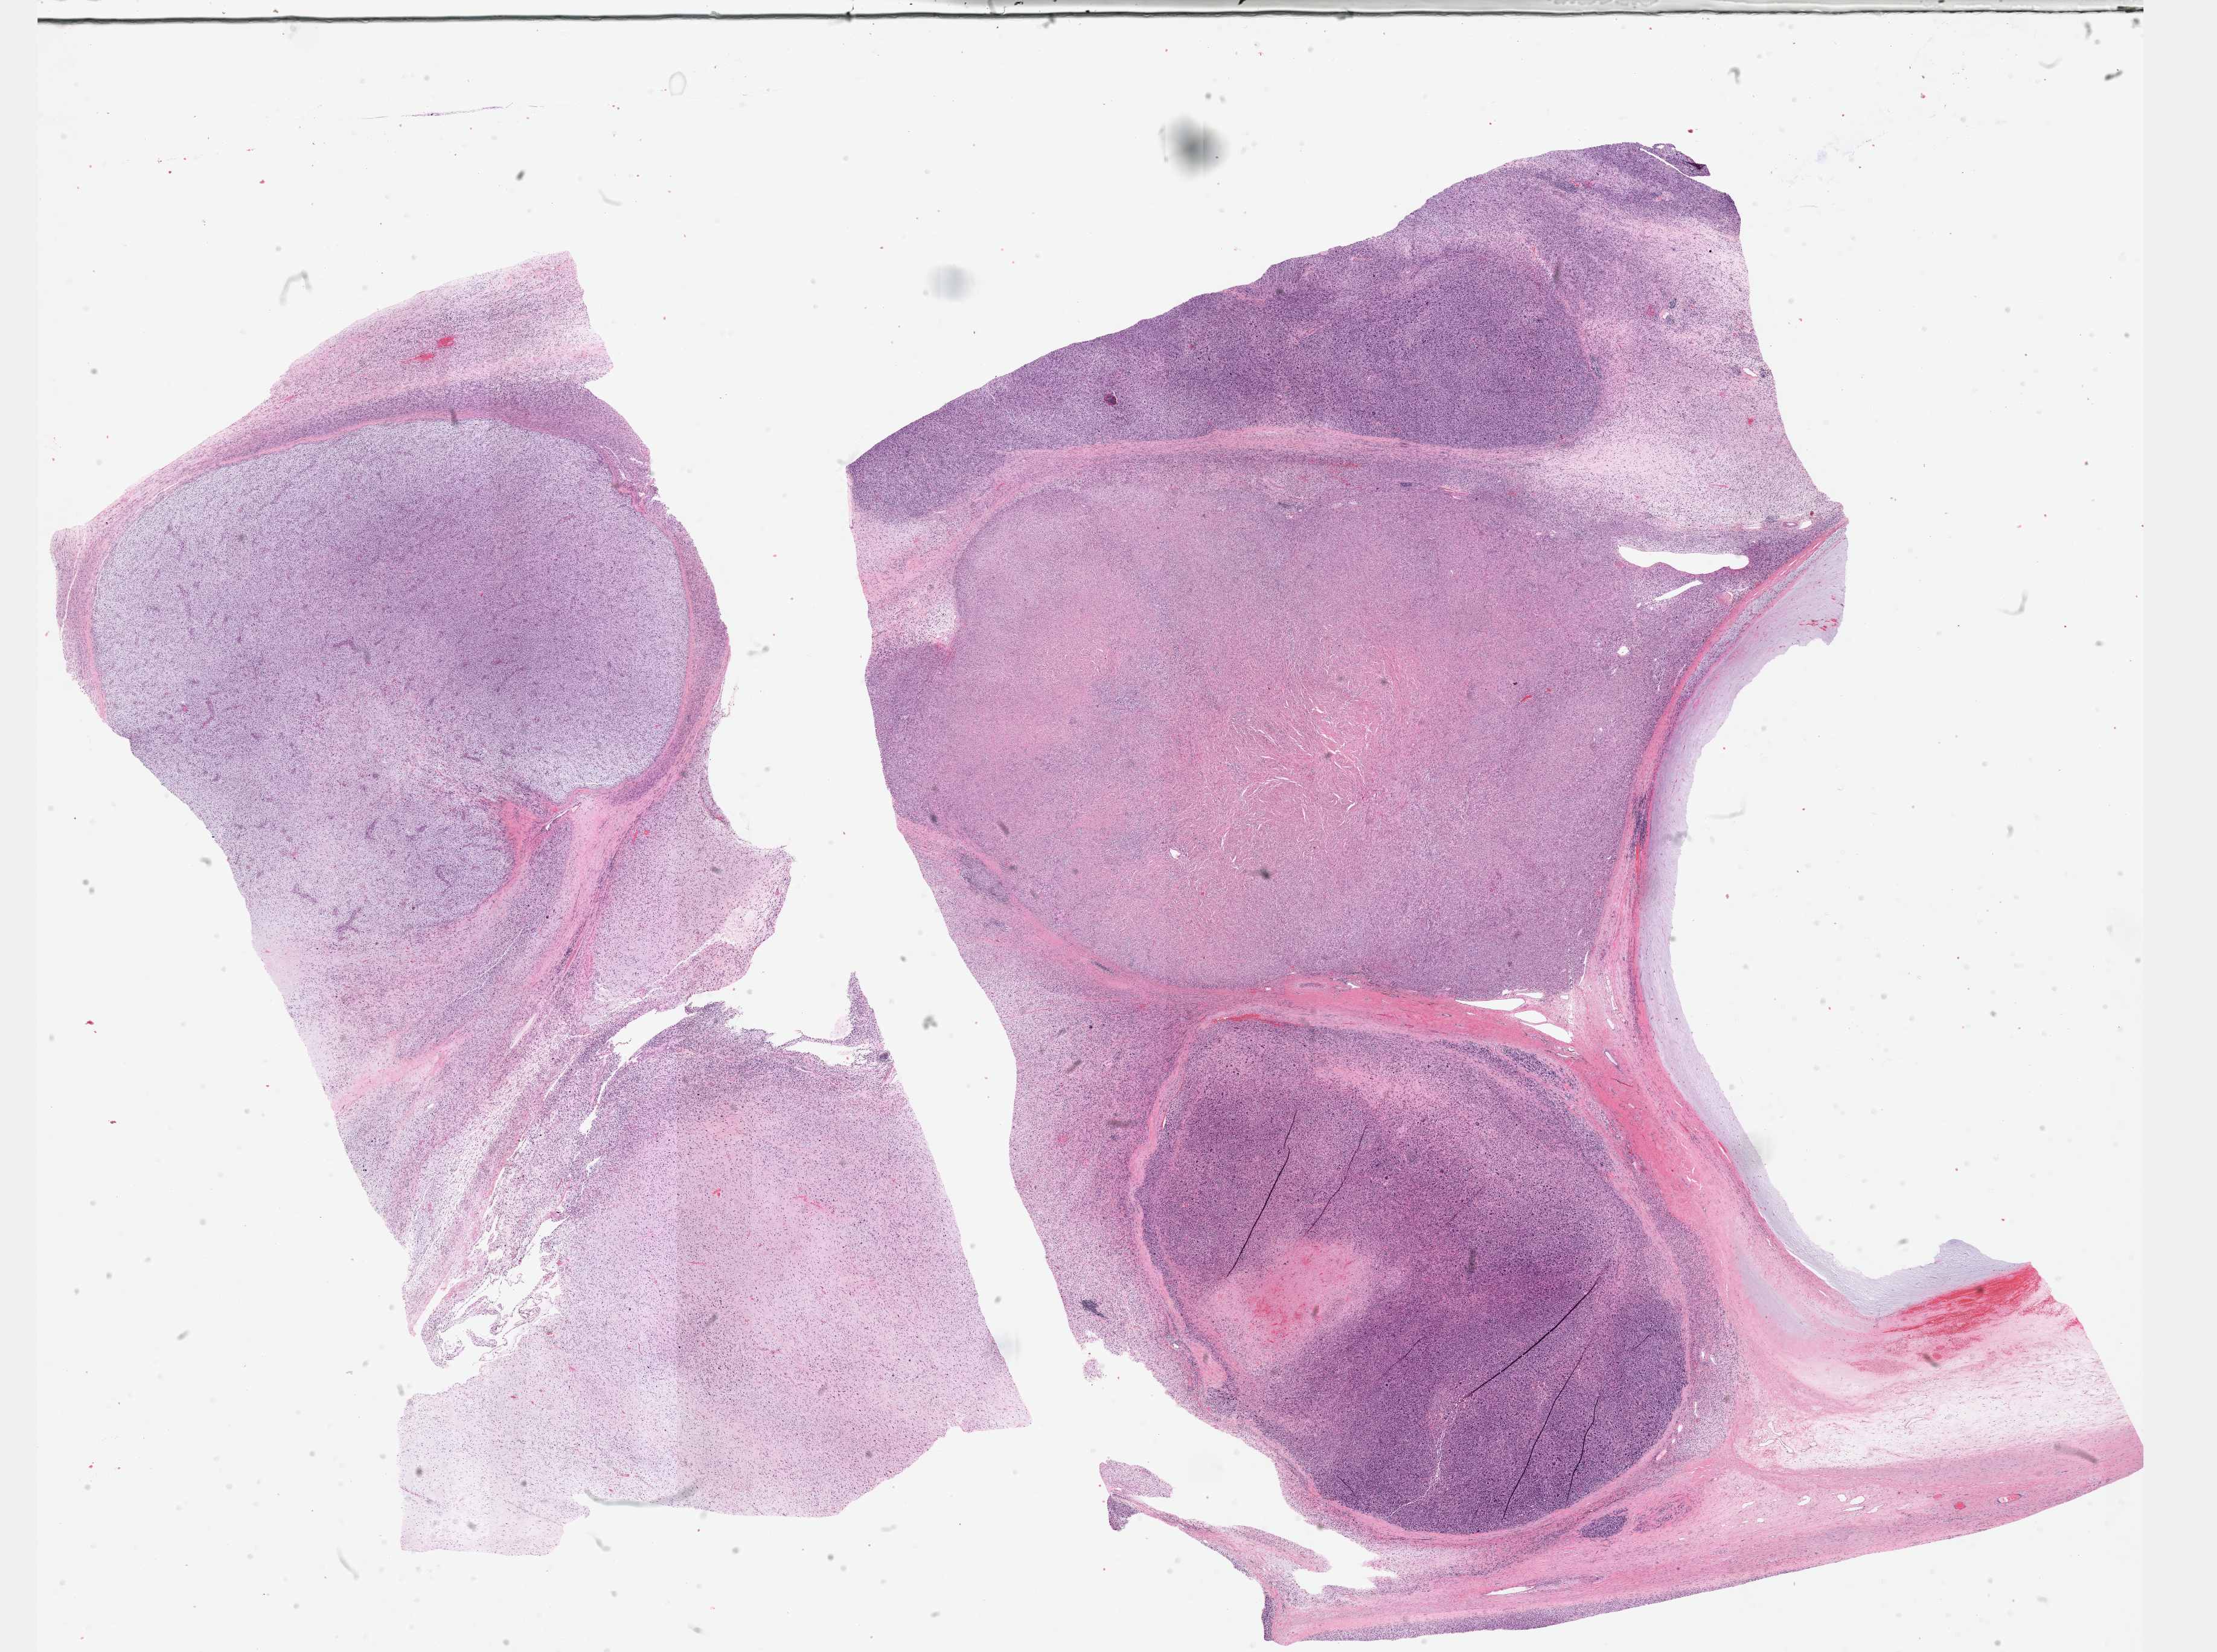
Digitized Hematoxylin and eosin (H&E) stained tissue section (whole slide), low-resolution overview of the scanned area, about 29.7 x 22.1 mm (acquisition: 40x scan); formalin-fixed paraffin-embedded (FFPE) diagnostic section; sample: primary tumour, connective, subcutaneous and other soft tissues. Male patient.
Pathologic diagnosis: Fibromyxosarcoma (connective, subcutaneous and other soft tissues of lower limb and hip).